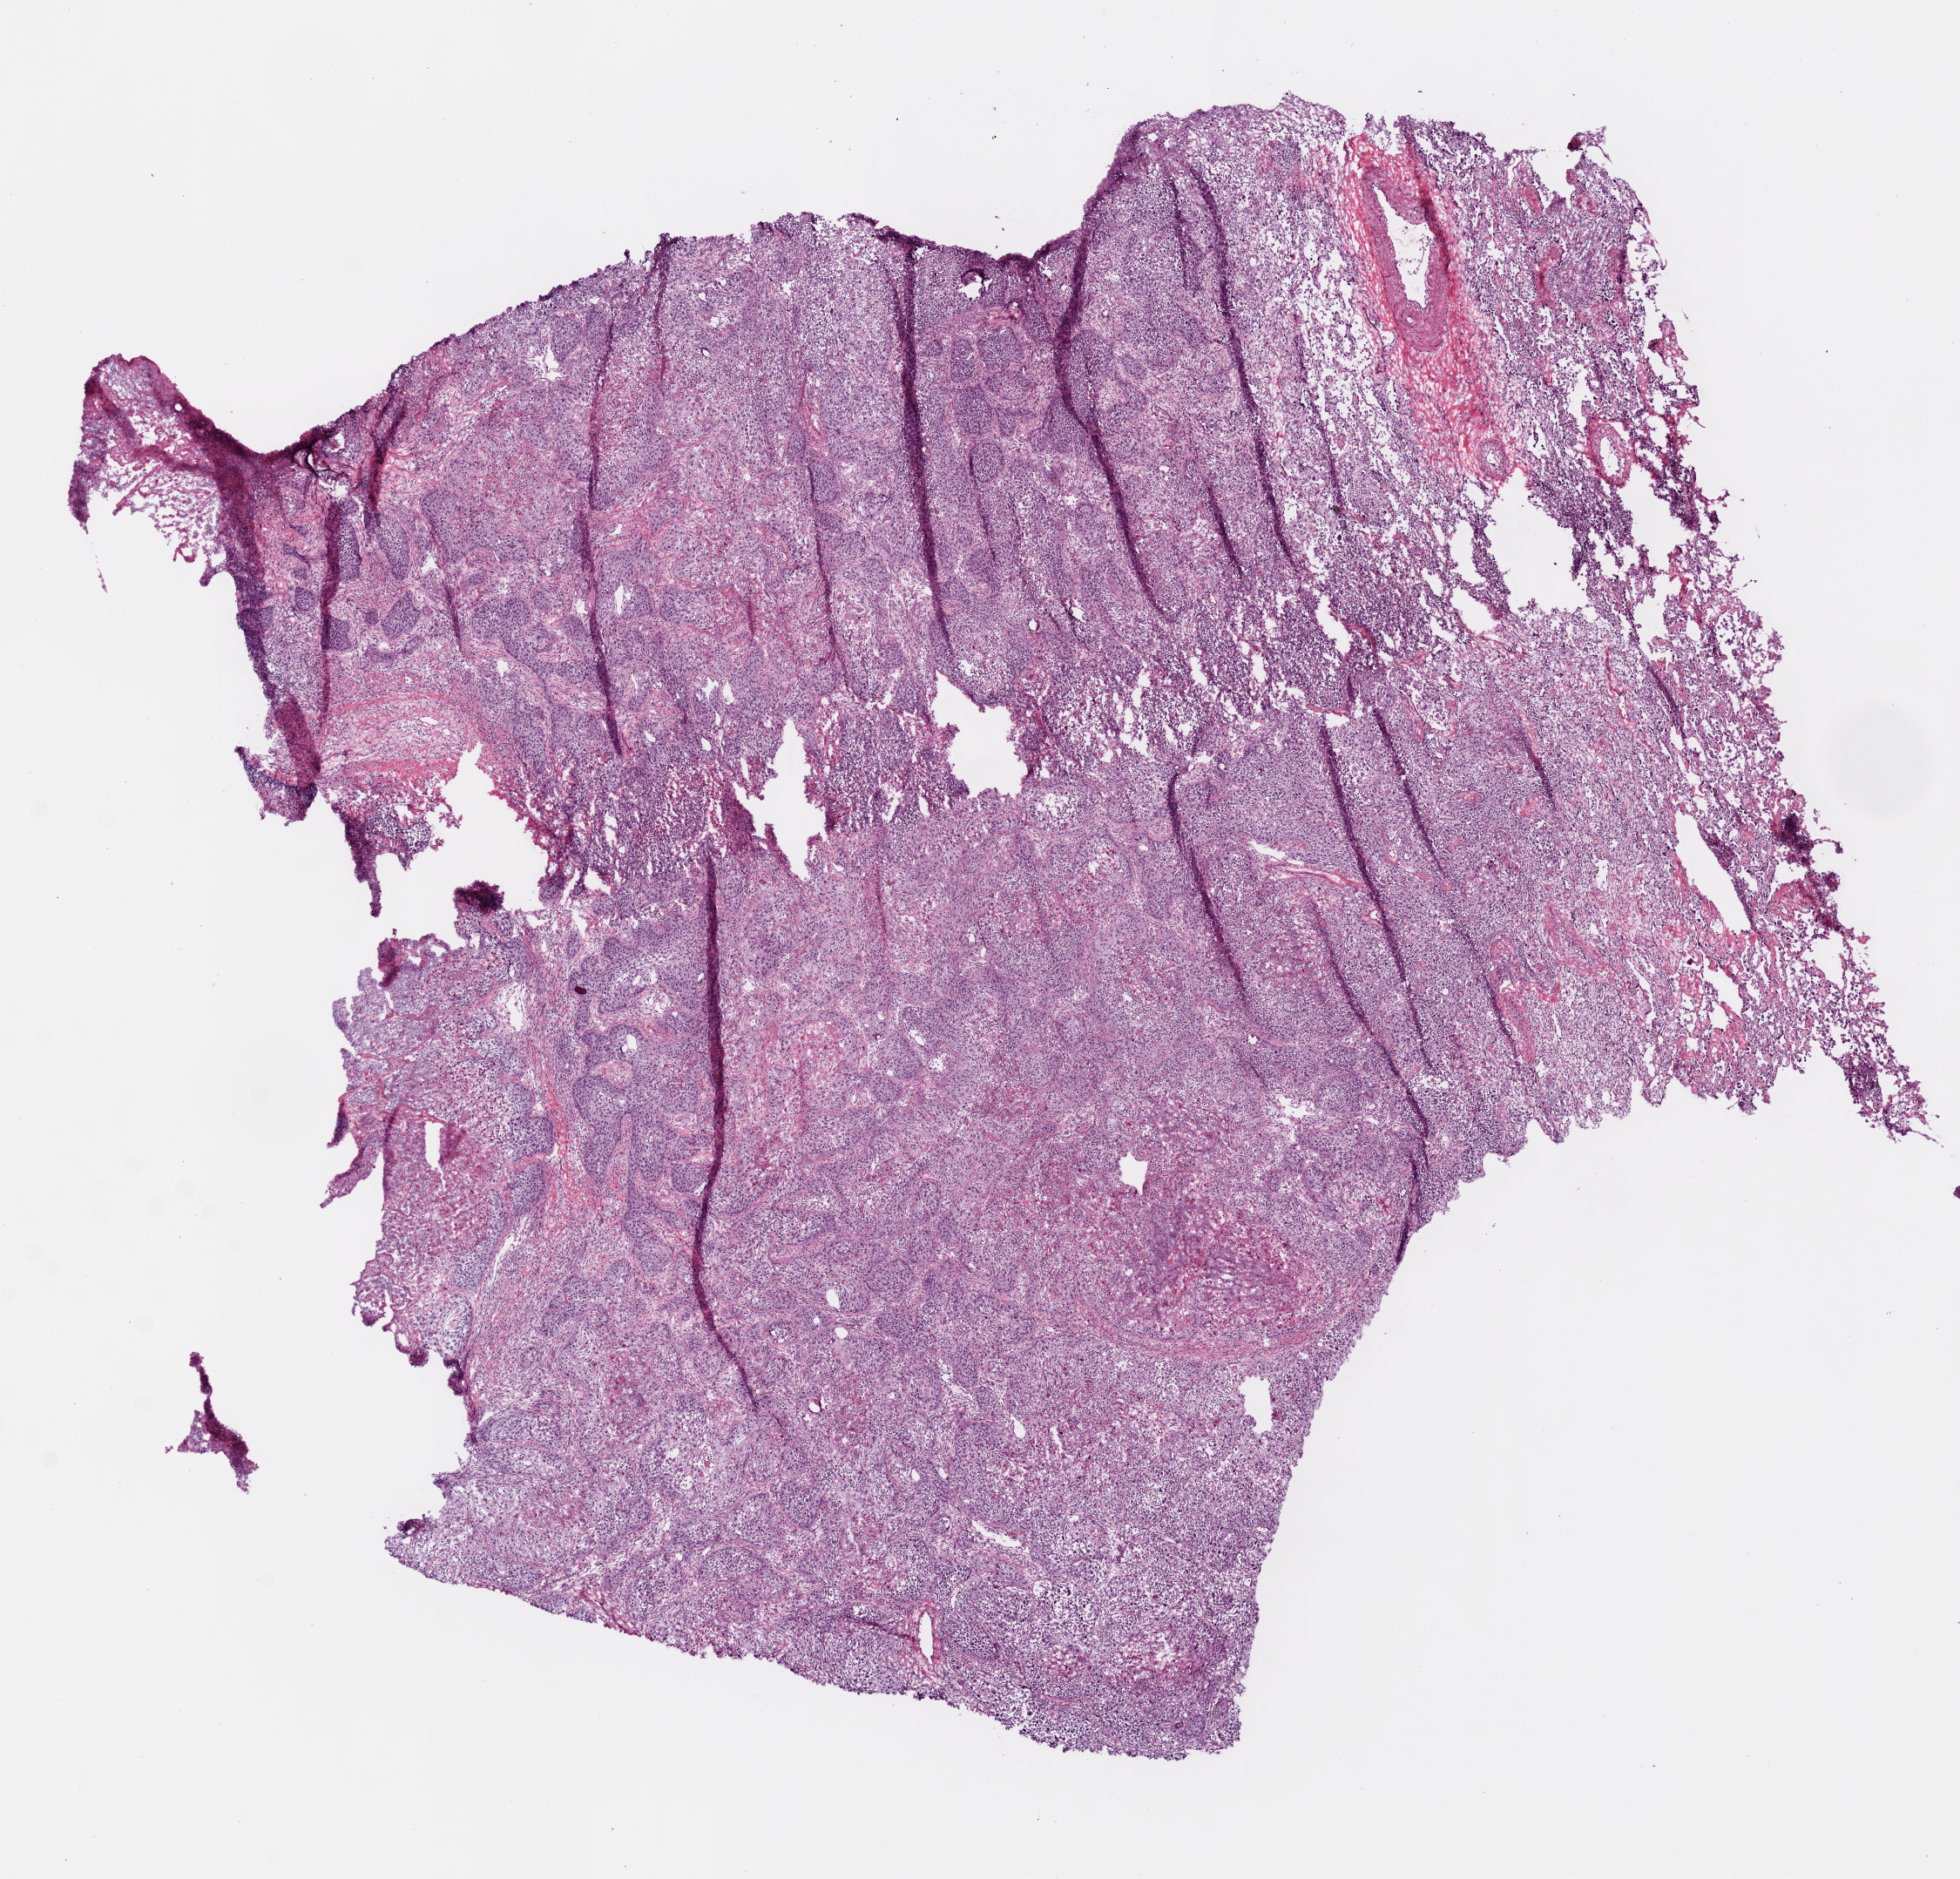
Digitized Hematoxylin and eosin (H&E) stained tissue section (whole slide), a low-resolution overview of the entire scanned area, about 9.0 x 8.7 mm (acquisition: 20x scan). Frozen section from the bottom of the tissue portion. Lung, primary tumour sample. Patient: female, age at initial diagnosis 62 years. Slide review estimates, as recorded: tumour cells 70%, tumour nuclei 70%, normal cells 0%, stromal cells 15%, necrosis 15%. Infiltration values recorded for this section: lymphocyte infiltration 5%.
• AJCC pathologic stage: IB
• histologic diagnosis: Squamous cell carcinoma, NOS